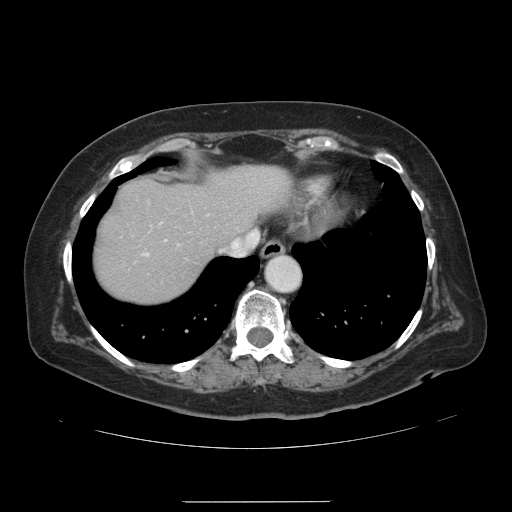
Contrast-enhanced abdominal CT, one axial slice; slice 117 of 141 in the series (ordered by position); intravenous contrast given; soft-tissue window (W 400 / L 40 HU); 2.5 mm slice thickness; 512 × 512 image matrix, field of view 393 × 393 mm. Female patient, age 74 years. Case-level facts recorded for this patient, not image findings: diagnosis: colorectal cancer liver metastases, imaged before liver resection; multiple liver metastases: yes; largest metastasis: 7 cm; chemotherapy before resection: no.
Annotated regions visible in this slice (manually delineated by an expert):
- hepatic veins: bounding box <220,238,251,254> (left, top, right, bottom; pixels)
- liver: <96,166,288,302>
- planned liver remnant (the part of the liver to remain after resection): <96,166,288,291>
- portal vein (with intrahepatic branches): <165,231,253,240>